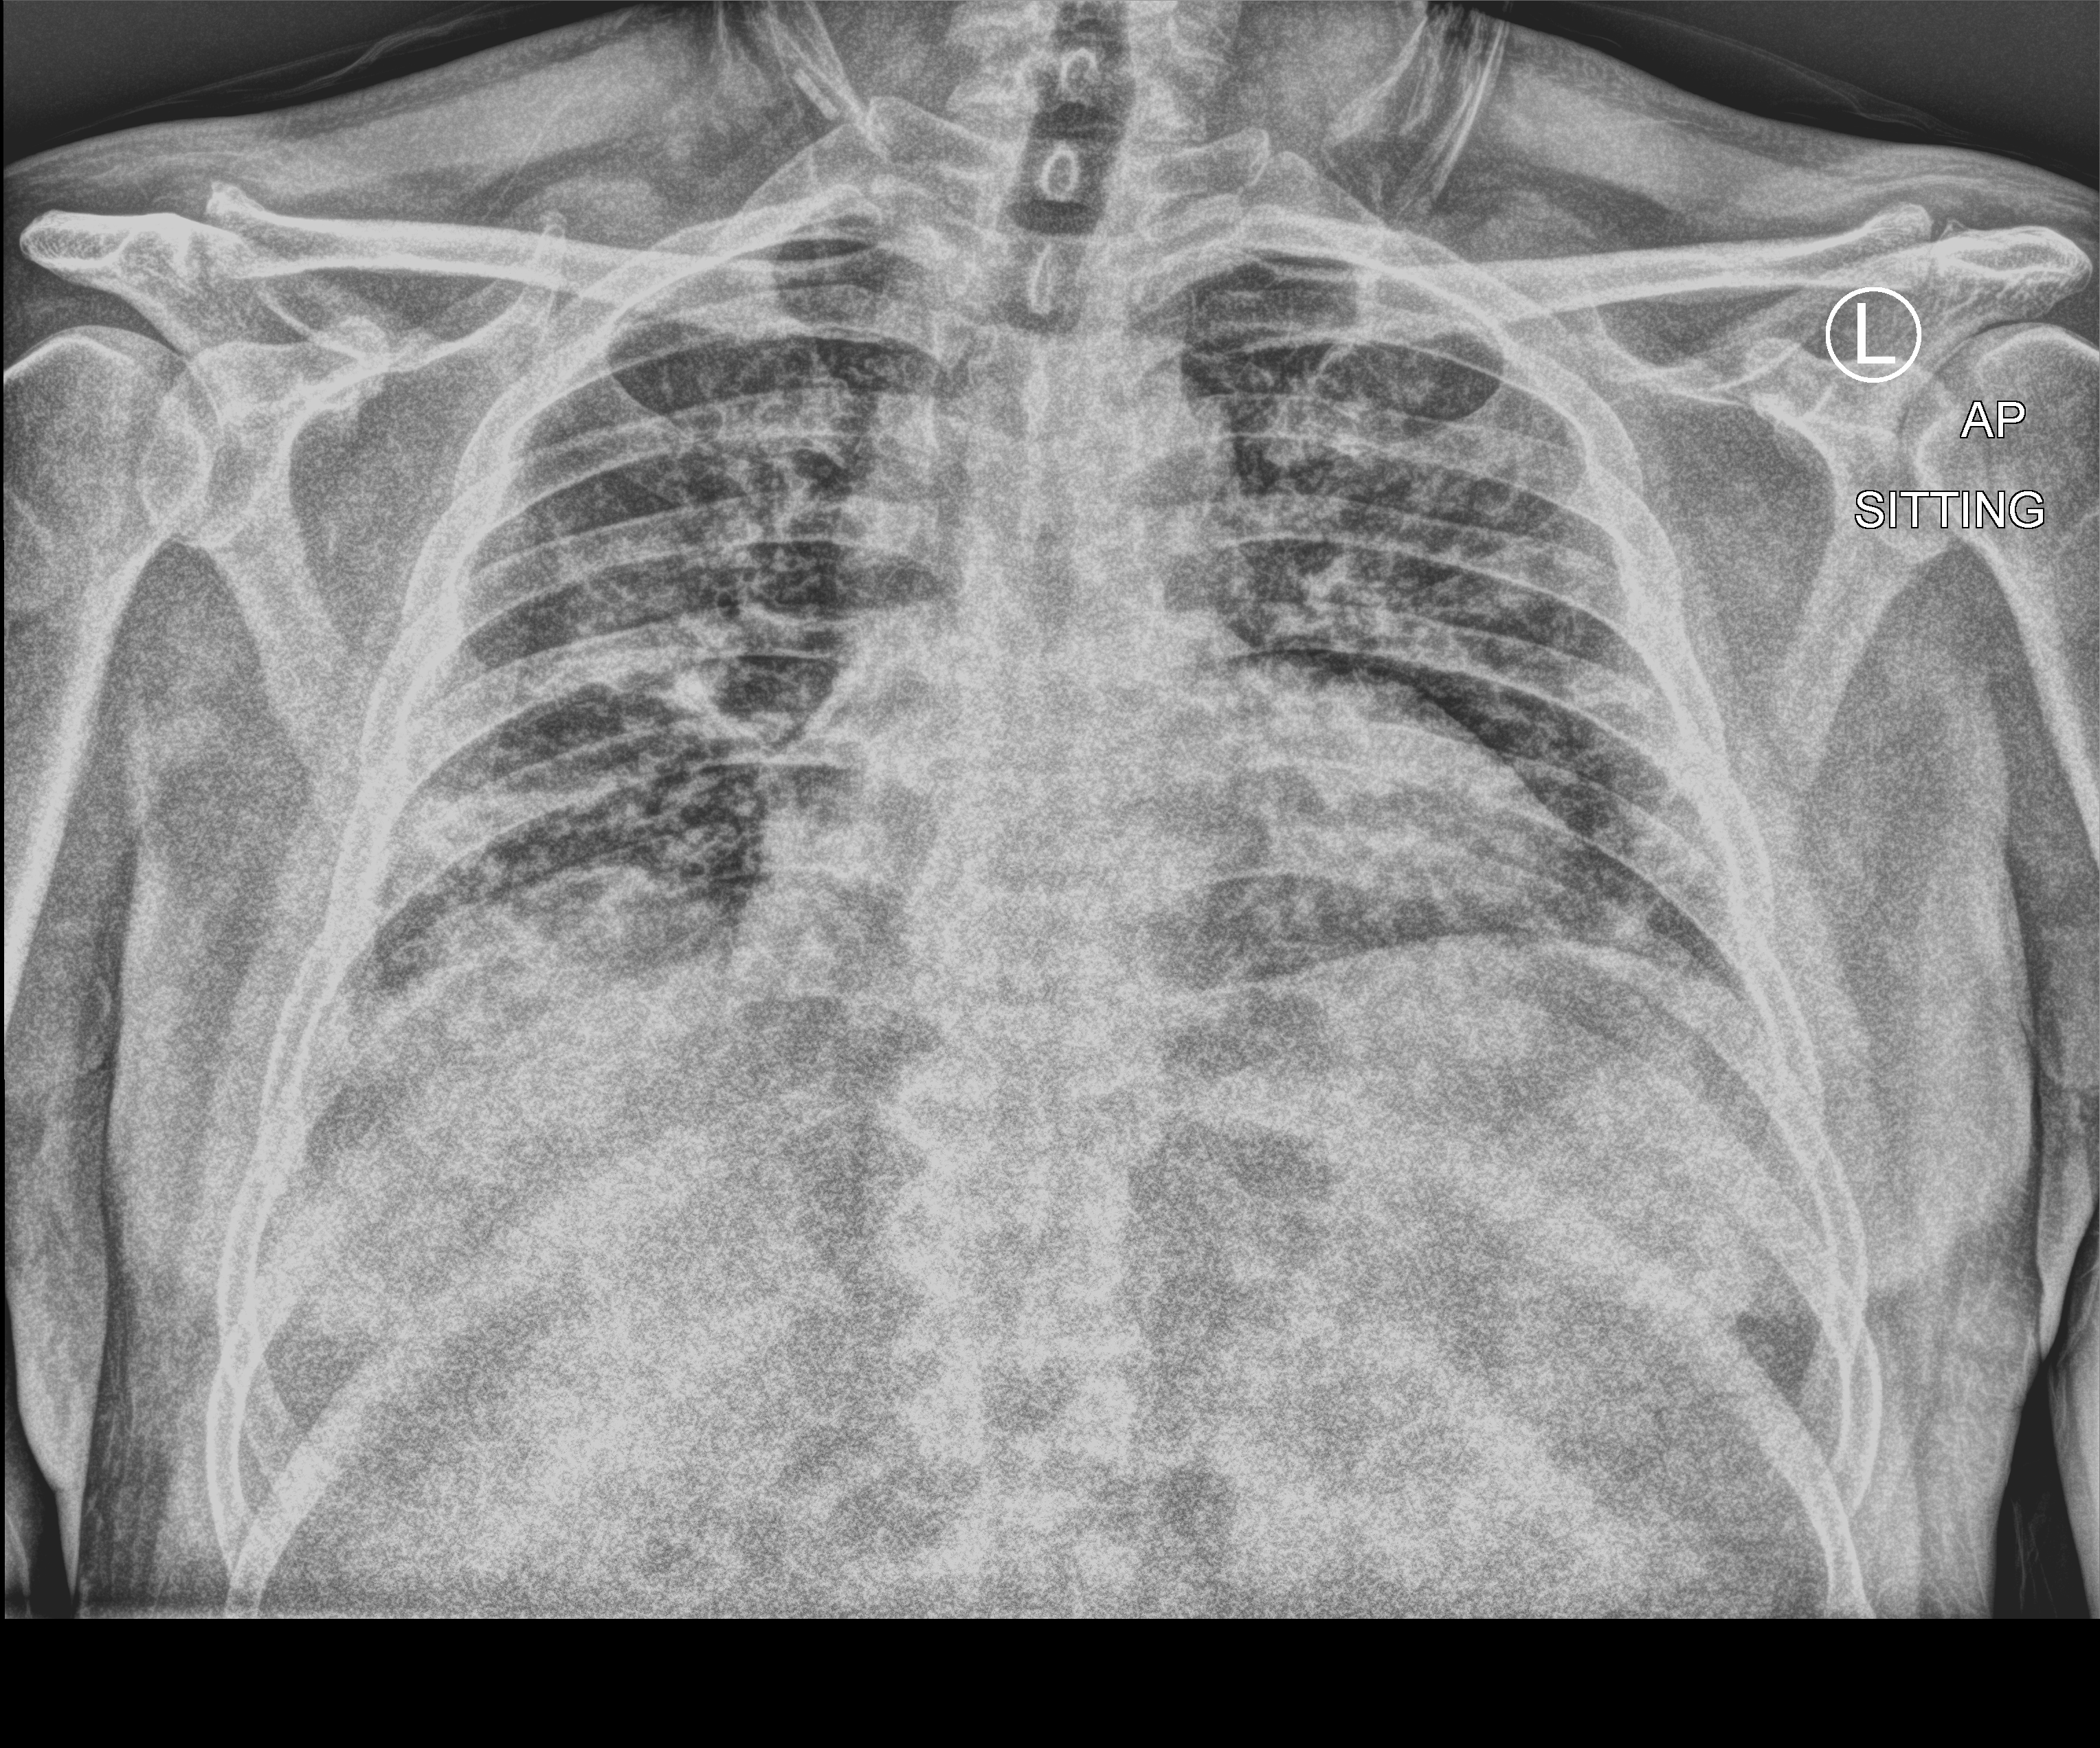
Portable chest radiograph; anteroposterior (AP) projection. Male patient hospitalised with COVID-19, age 18–59 years.
From the hospital-stay record, not from the radiograph (when in the stay this image was taken is not recorded):
- admitted to intensive care during this hospital stay: no